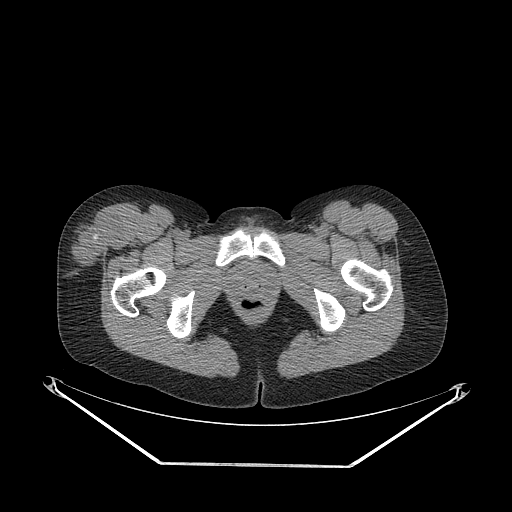
CT of an extremity soft-tissue mass (from a PET/CT study), one axial slice; position 59 of 267 along the scan axis; reconstruction kernel STANDARD; soft-tissue window (W 400 / L 40 HU); 3.75 mm slice thickness; 512 × 512 image matrix. Female patient. Case-level facts recorded for this patient, not image findings: histological type: synovial sarcoma; grade: intermediate; site of the primary tumour: right thigh.
Outlined on this slice (expert contour drawn on MRI and transferred to this co-registered scan by the dataset authors):
- gross tumour volume including surrounding oedema: bounding box [x1, y1, x2, y2] px = [71, 212, 122, 268]
- gross tumour volume (mass): [71, 212, 122, 268]